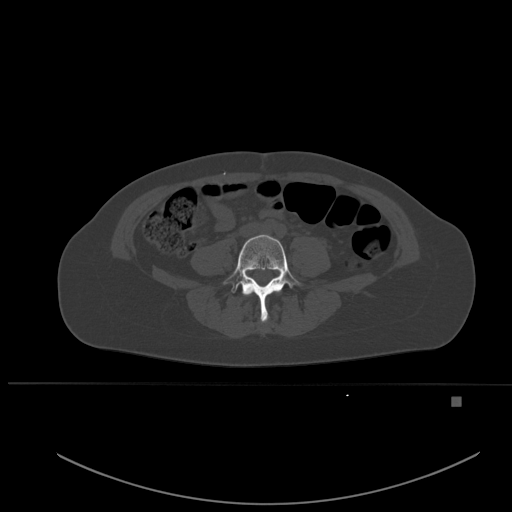
CT including the spine, one axial slice; slice 174 of 651 in the series (ordered by position); bone window (W 1800 / L 400 HU); 1.5 mm slice thickness; 512 × 512 image matrix, field of view 443 × 443 mm. Patient: female, 49 years. Case-level facts recorded for this patient, not image findings: primary cancer: breast; vertebrae with lytic lesions (as recorded): L3, T12, L4.
Structures marked on this image (semi-automatic segmentation, software-assisted and operator-edited):
- L3 vertebra: box from (x=244, y=290) to (x=281, y=295) px
- L4 vertebra: (x=223, y=234)–(x=301, y=322)